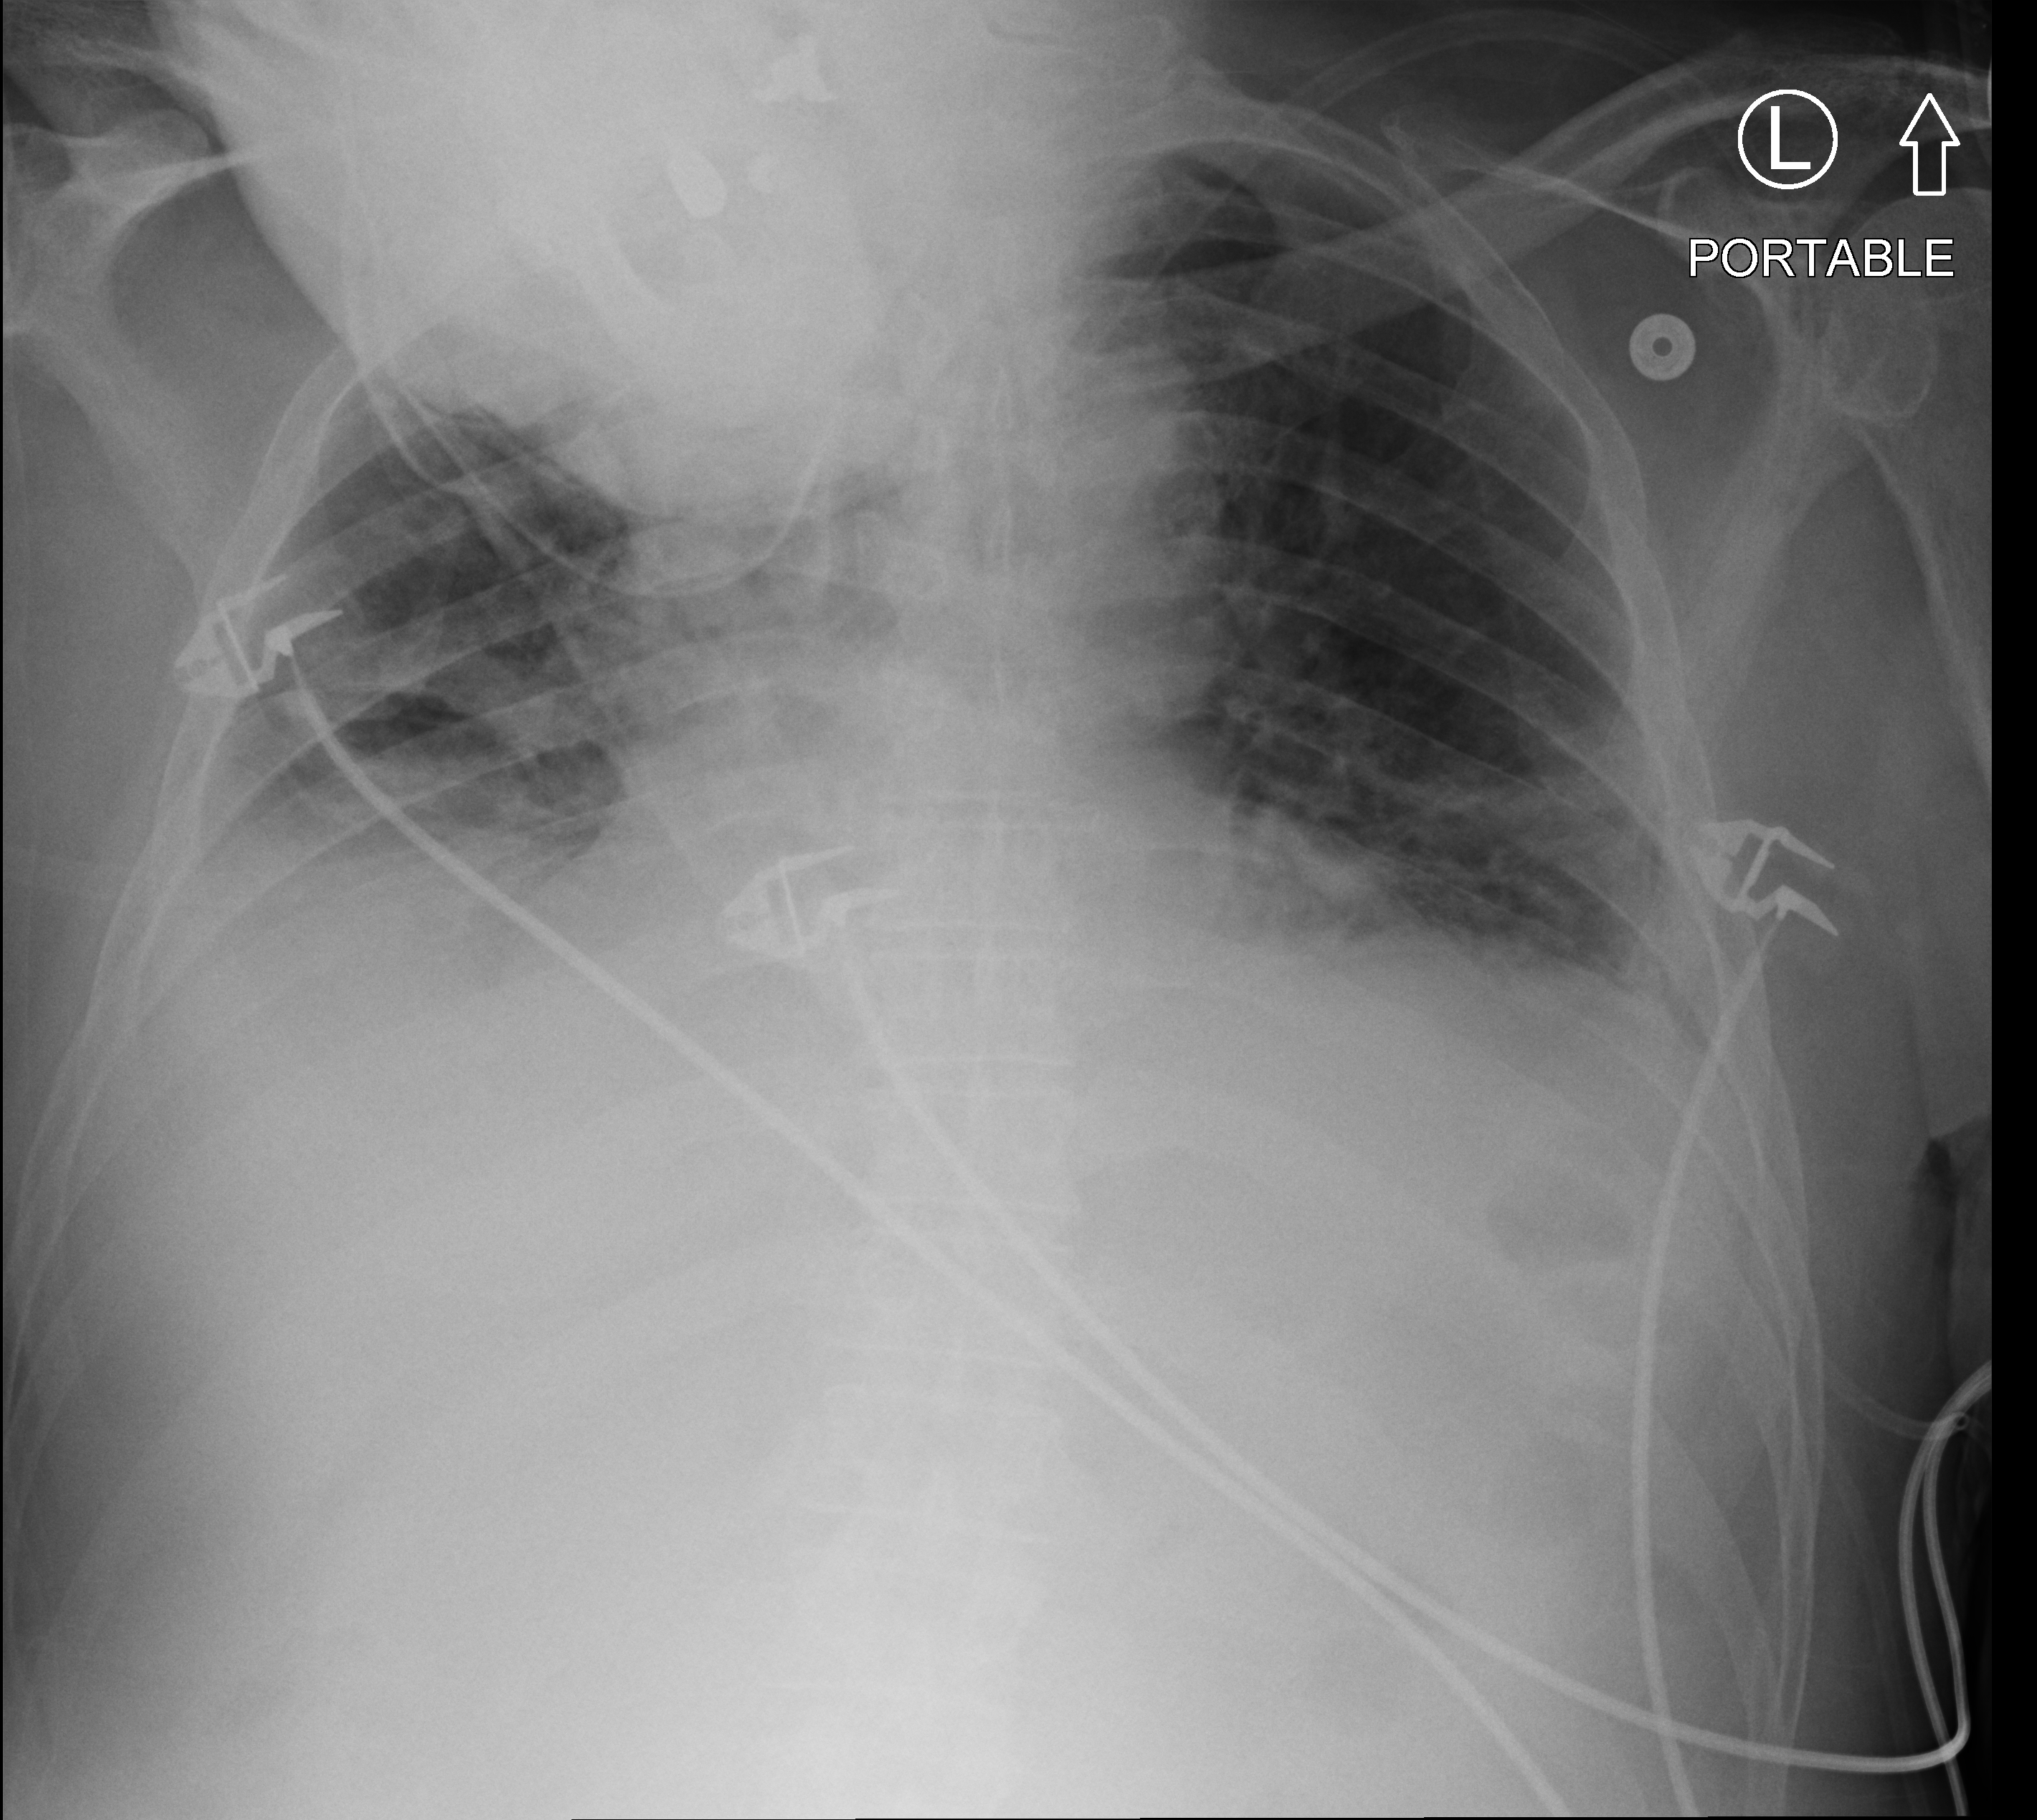
Chest X-ray (portable). Patient hospitalised with COVID-19; male, aged 60–74 years.
Hospital-stay facts (about this admission, not read from this image; timing relative to this image not recorded):
- mechanically ventilated during this hospital stay: no